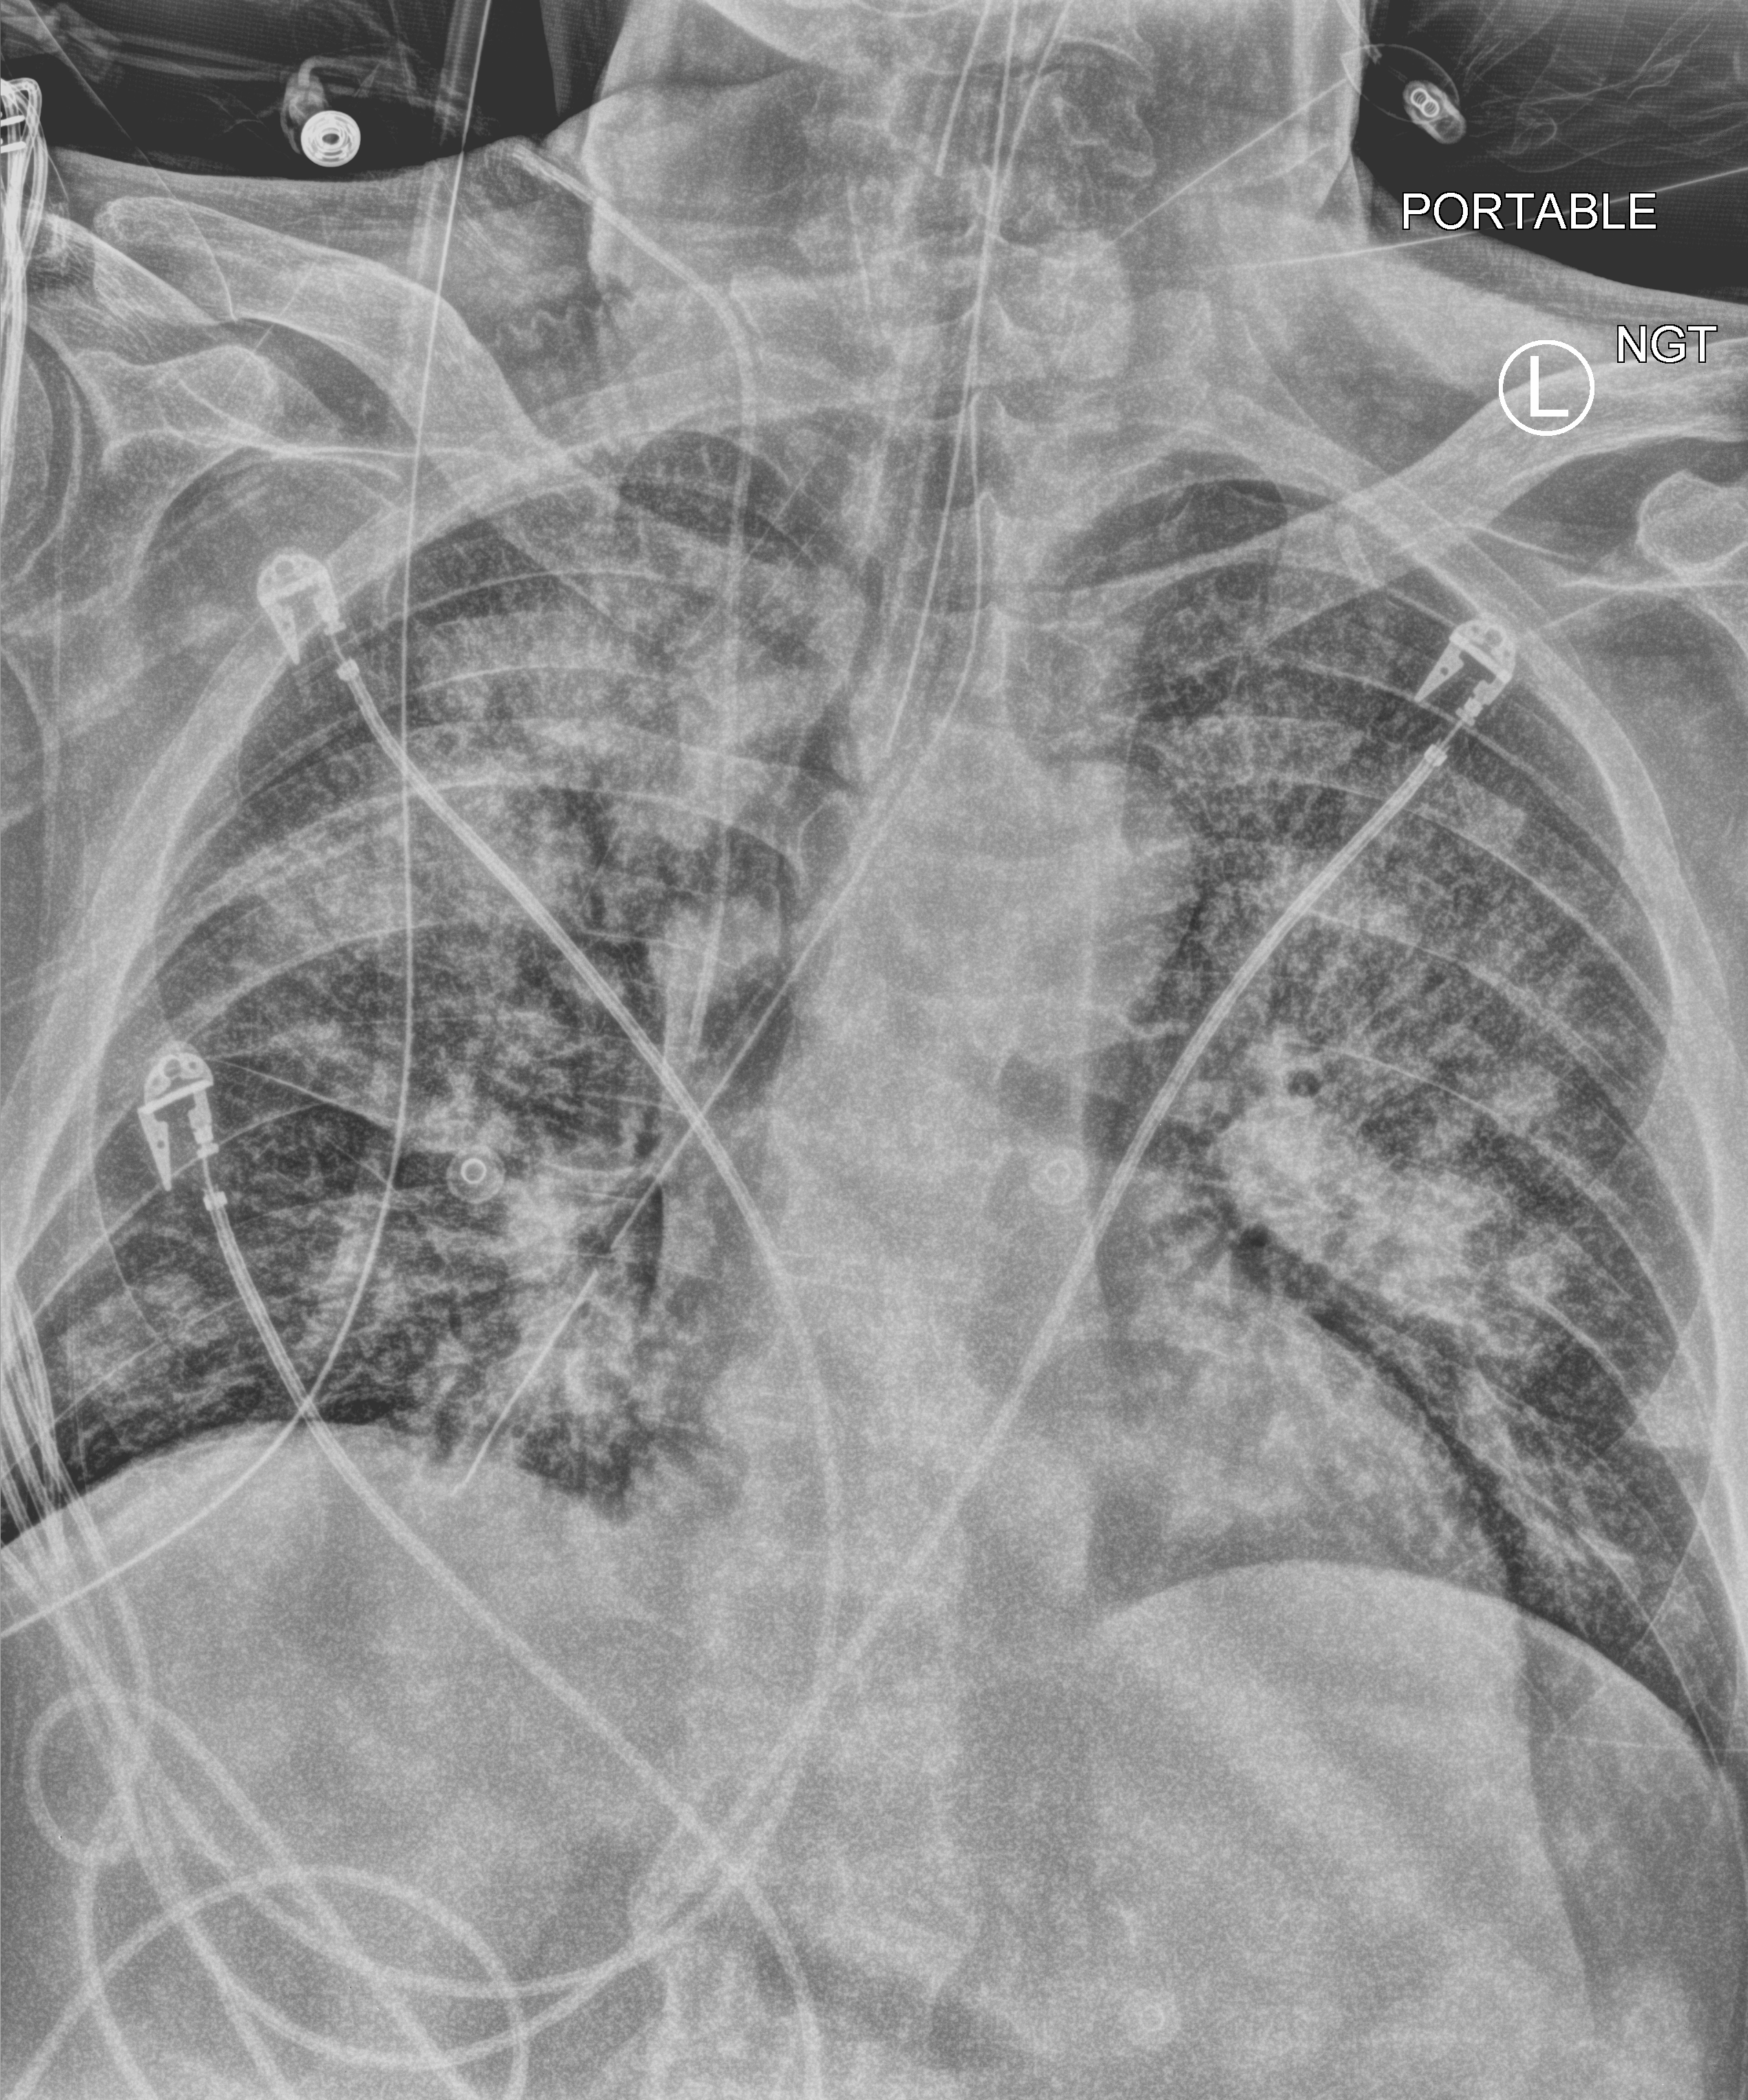
Chest X-ray (portable), anteroposterior (AP) projection. Patient hospitalised with COVID-19; male, aged 75–90 years.
Hospital-stay facts (about this admission, not read from this image; timing relative to this image not recorded): admitted to intensive care during this hospital stay: yes; smoking status (admission record): never; mechanically ventilated during this hospital stay: yes.